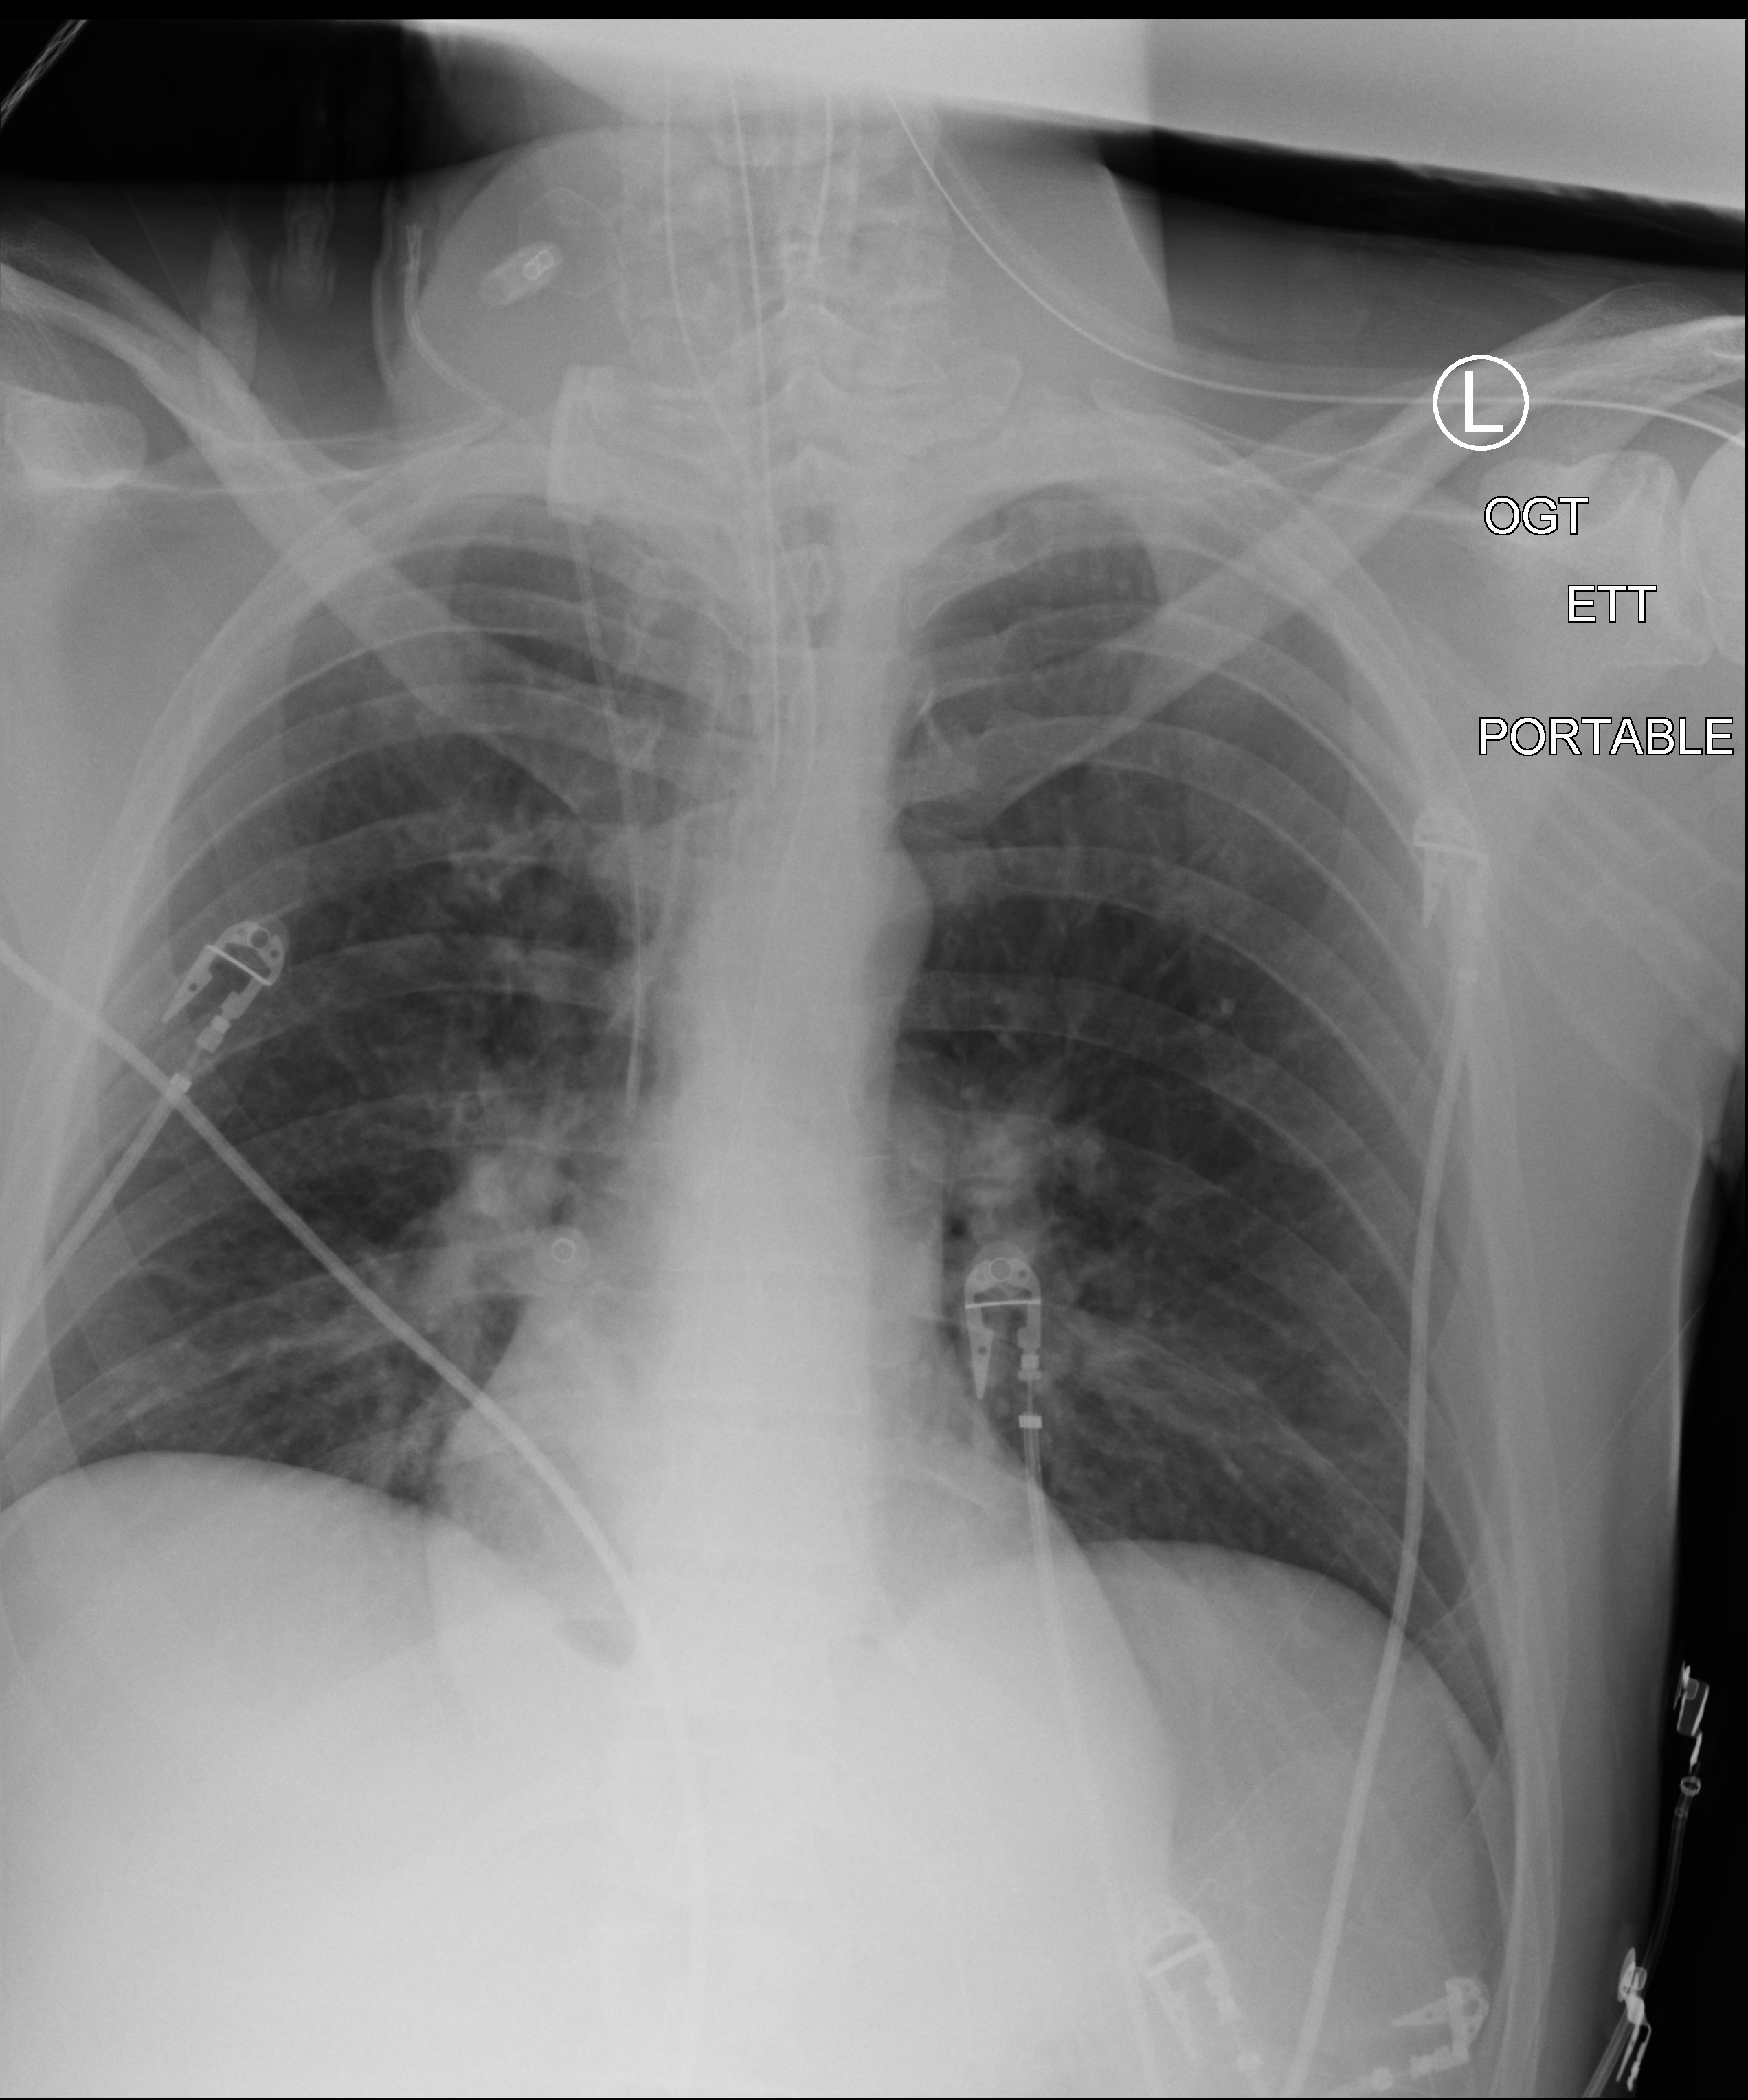
Portable chest radiograph. Male patient hospitalised with COVID-19, age 18–59 years.
Admission-level facts for this patient (not findings on this image; timing relative to this image not recorded):
- mechanically ventilated during this hospital stay: yes